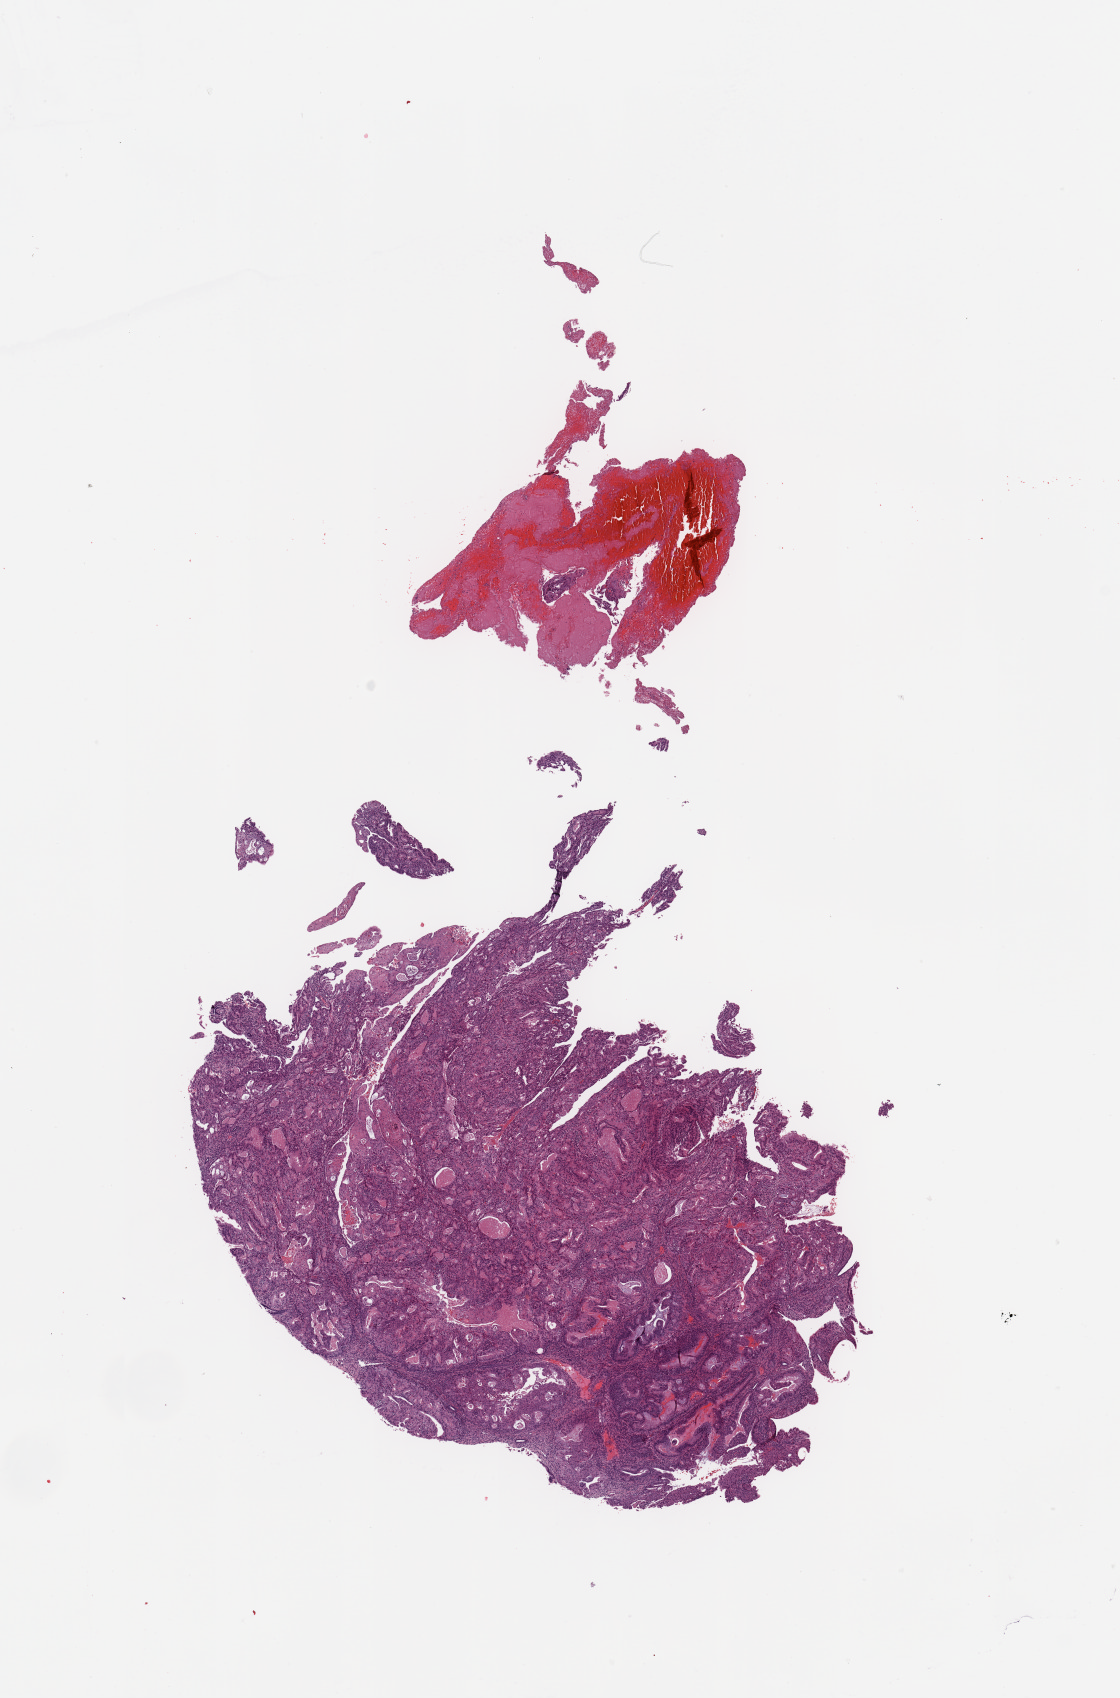
Digitized Hematoxylin and eosin (H&E) stained tissue section (whole slide), whole scanned area (about 8.9 x 13.4 mm, acquisition: 20x scan) shown as a low-resolution overview. Uterus, tumour tissue. Patient: female, age 54 years. Histologic grade: G2 (moderately differentiated).
Diagnosis: Endometrioid adenocarcinoma, NOS. AJCC pathologic stage: IIIB.